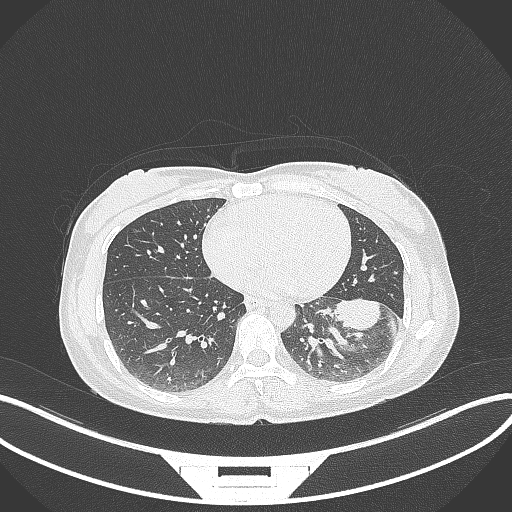
Chest CT, one axial slice; slice 22 of 244 in the series (ordered by position); lung window (W 1500 / L -600 HU); 1 mm slice thickness; 512 × 512 image matrix, field of view 400 × 400 mm. Female patient, age 41 years. Case-level facts recorded for this patient, not image findings: clinical TNM (as recorded): T2a N3 M1b.
Outlined on this slice (bounding box drawn by a radiologist):
- lung tumour (recorded histology: adenocarcinoma): bounding box (x1, y1, x2, y2) in pixels: (329, 299, 393, 336)